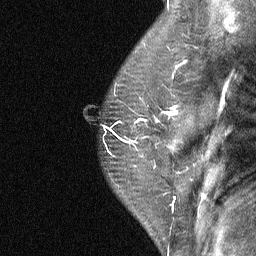
Breast MRI (dynamic contrast-enhanced), one sagittal slice; position 50 of 64 along the scan axis; dynamic contrast-enhanced study with each time point stored as its own series, time point 2 of 4 at this slice position (early post-contrast, ordered by acquisition time); 1.5 T; TE 4.8 ms, TR 27 ms; 2 mm slice thickness; 256 × 256 image matrix, field of view 180 × 180 mm. Female patient, age 50 years. Case-level facts recorded for this patient, not image findings: setting: breast cancer imaged before/during neoadjuvant chemotherapy; receptor status: HER2-positive.
Annotated regions visible in this slice (semi-automatically segmented with operator editing):
- analysis volume of interest (the breast-tissue region the enhancement analysis was run in; not a lesion): bounding box <123,91,189,177> (left, top, right, bottom; pixels)
- tumour enhancement mask (voxels above the 90 % enhancement threshold inside the analysis volume of interest): <123,108,177,142>